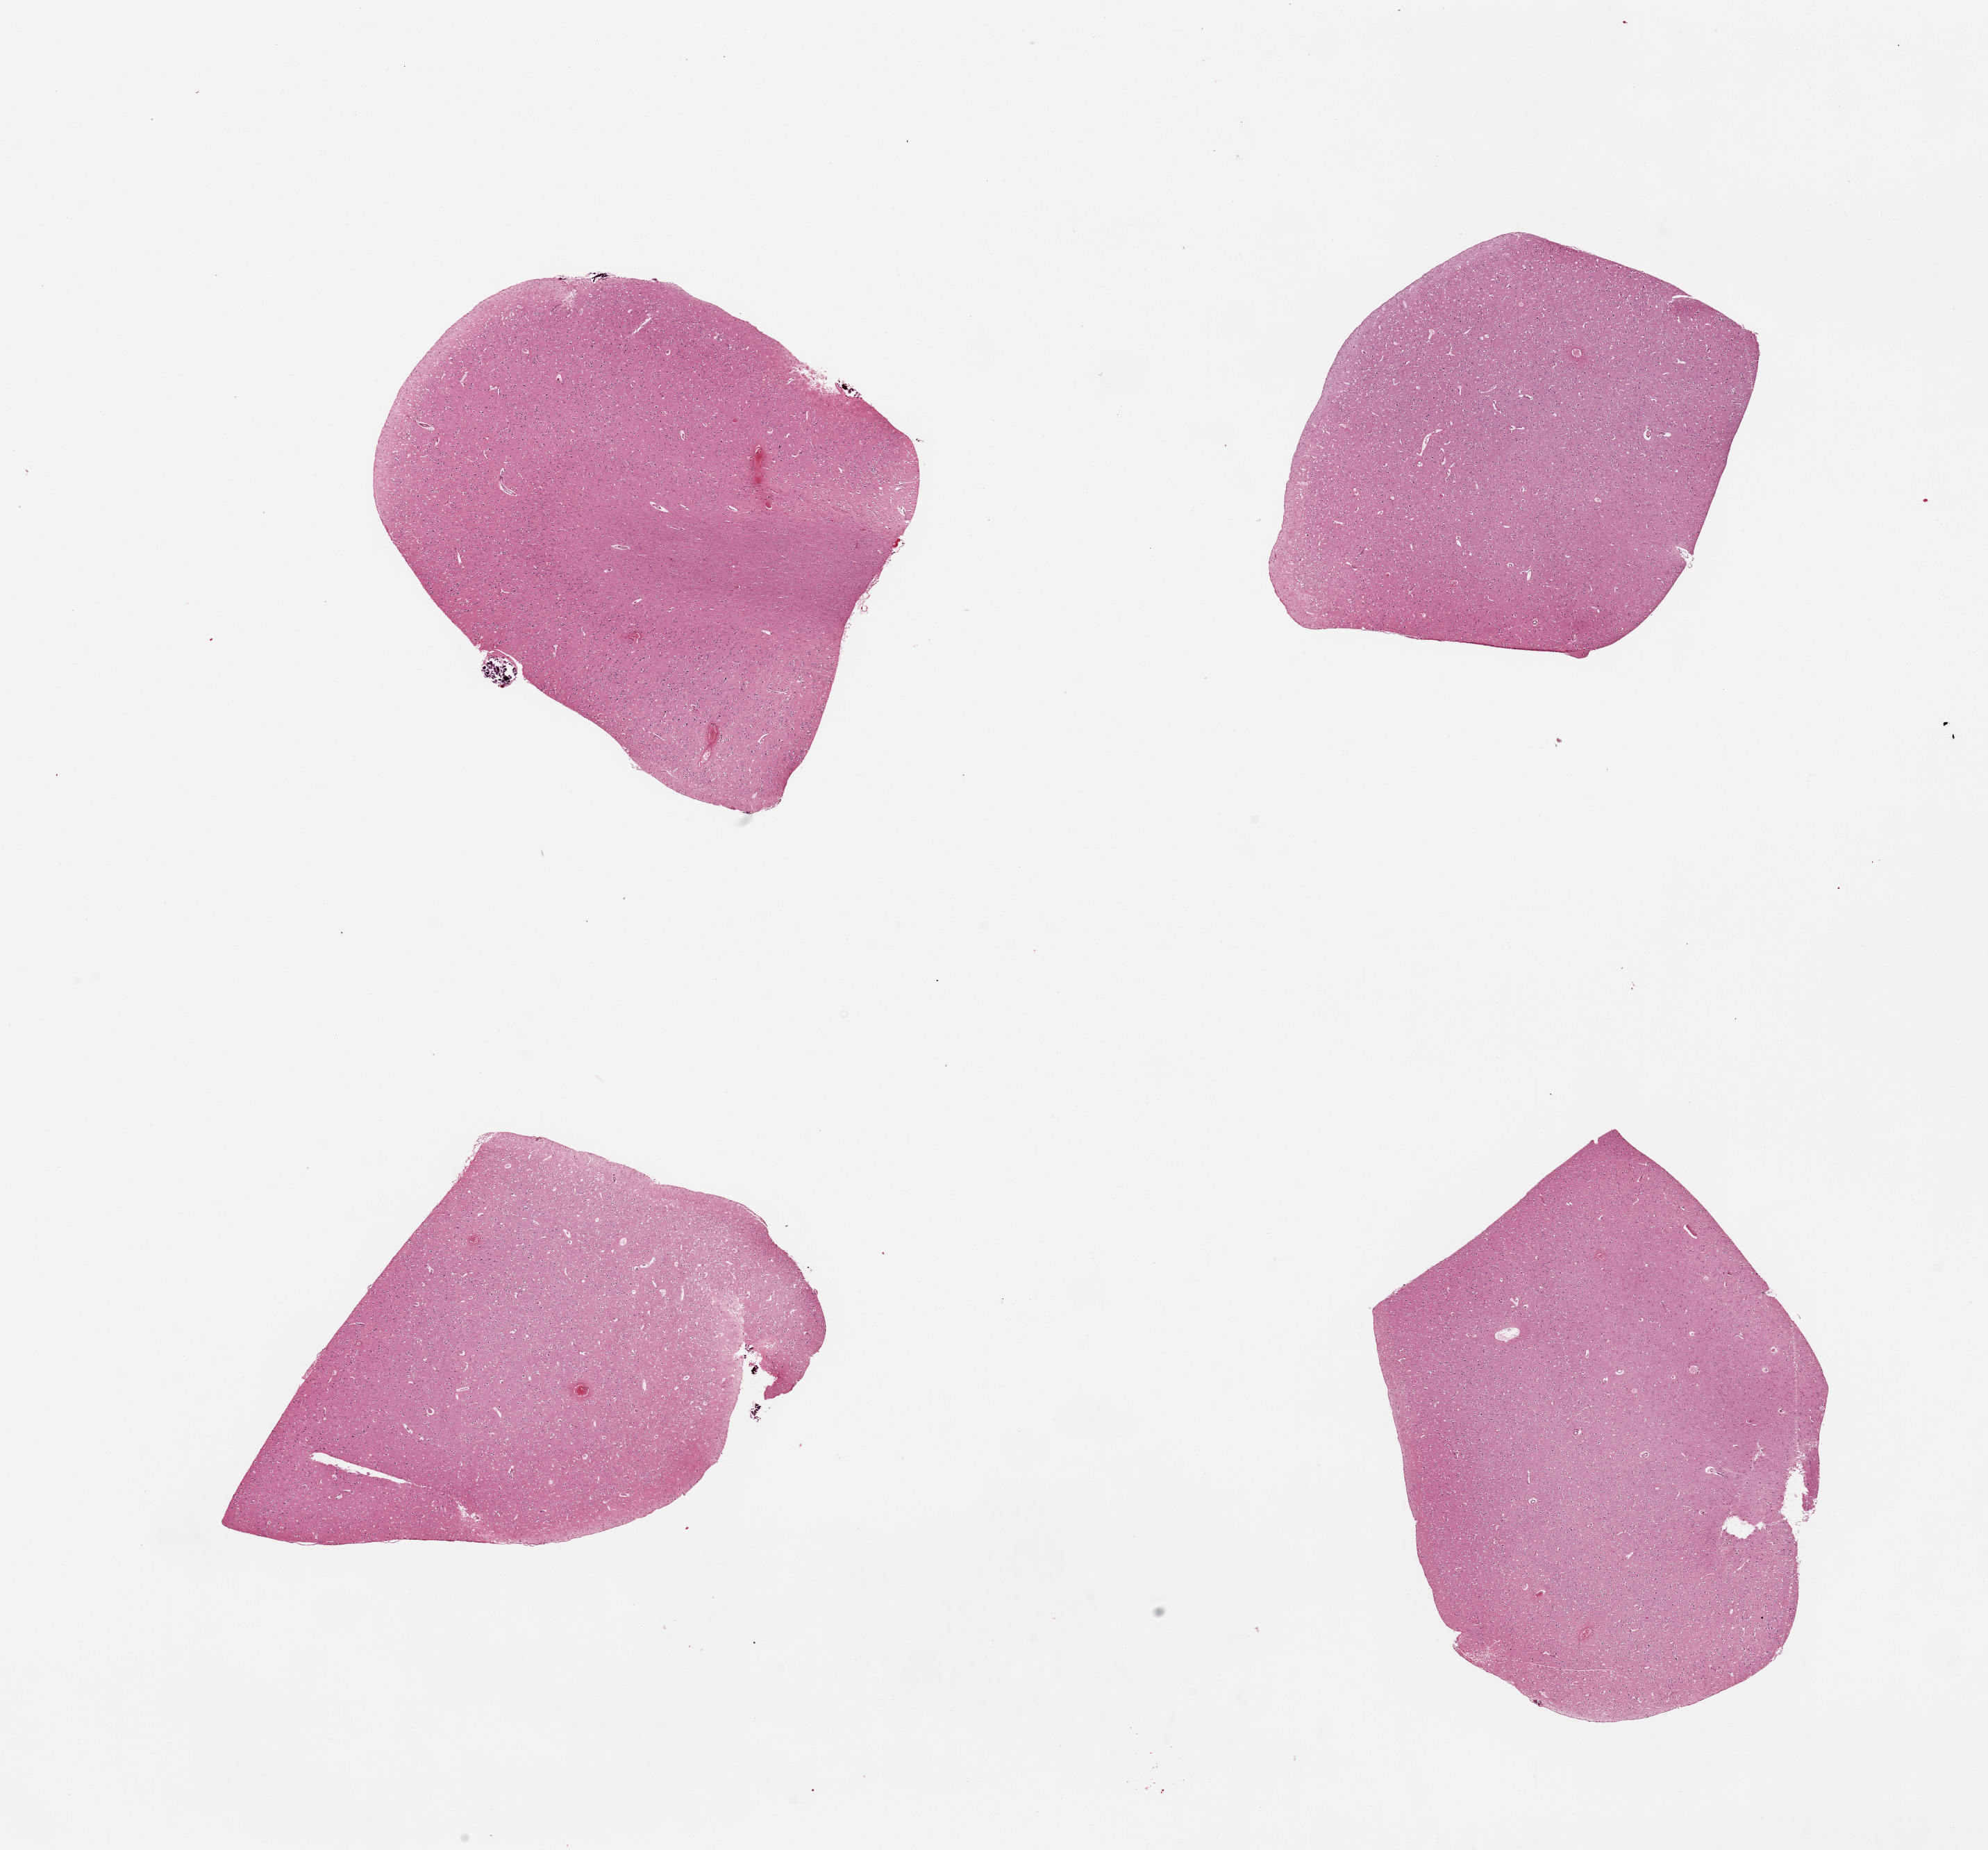
Whole-slide image, H&E stain, brightfield — shown as a low-resolution overview of the whole scanned area (about 22.6 x 21.1 mm); PAXgene-fixed paraffin-embedded (PFPE) section; sampled site (target tissue): cerebral cortex; tissue donor sample.
Reviewer comment on this tissue sample: 4 pieces.